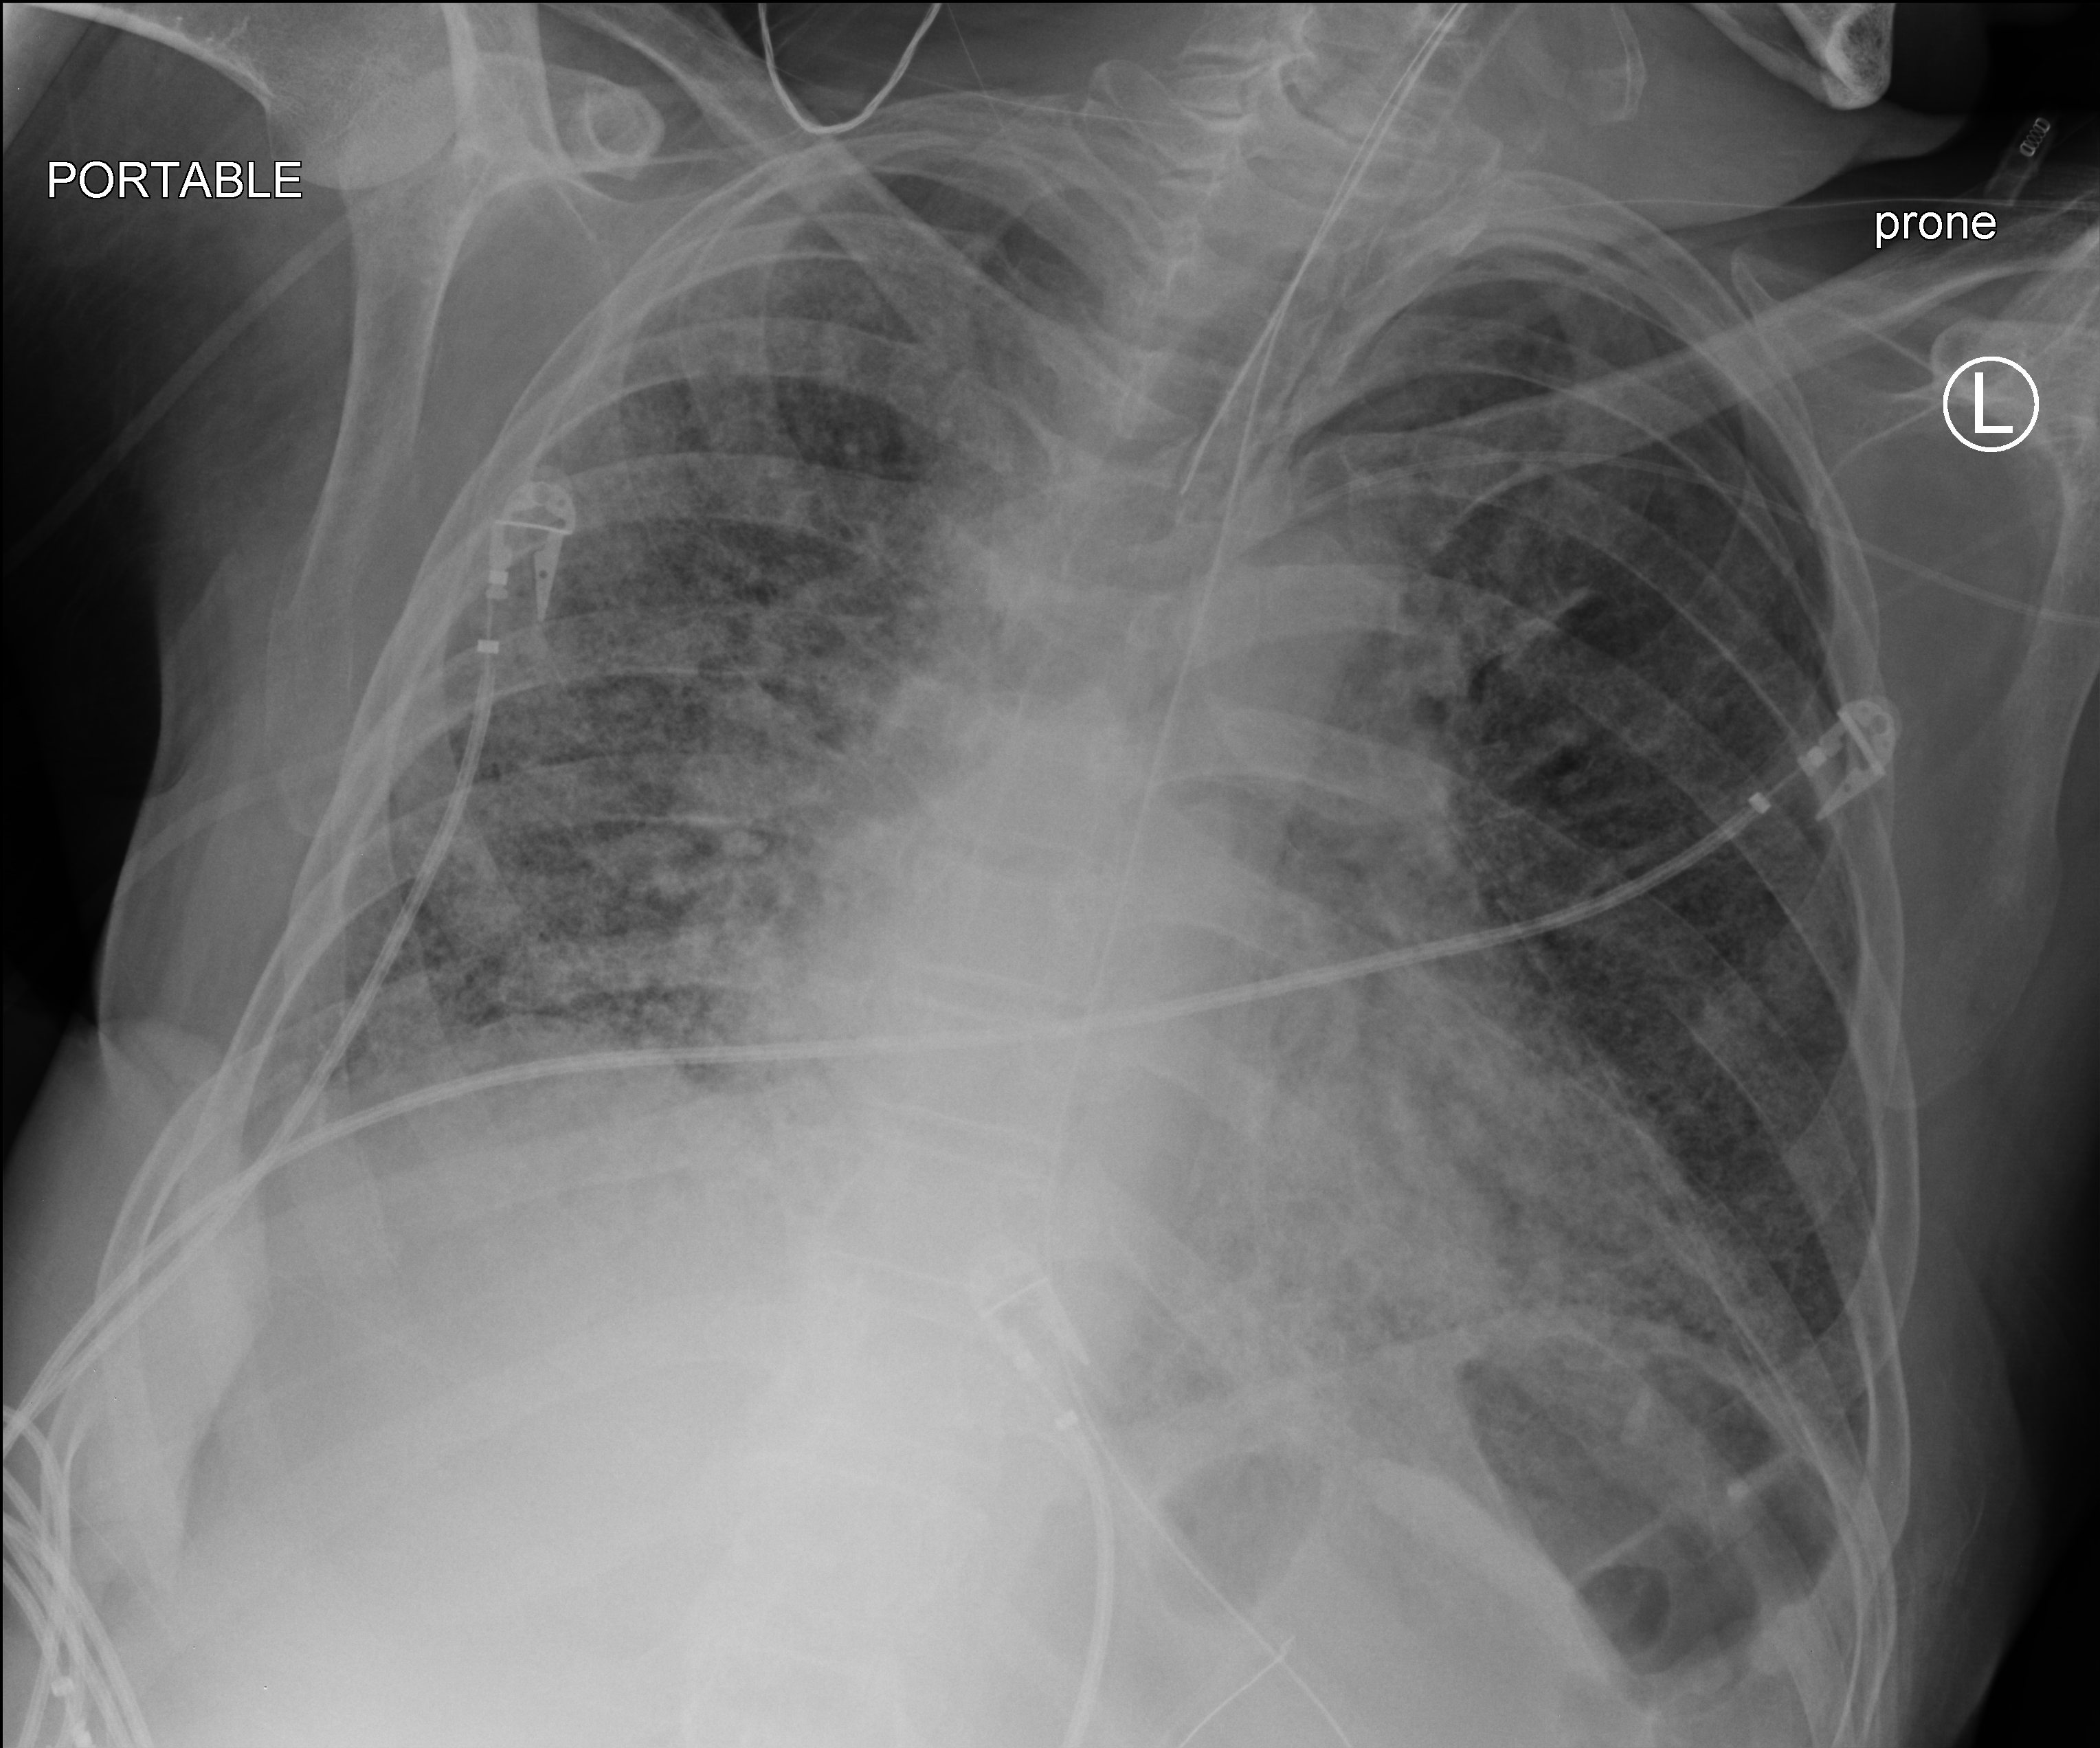
Portable chest radiograph; anteroposterior (AP) projection. Male patient hospitalised with COVID-19, age 60–74 years.
Admission-level facts for this patient (not findings on this image; timing relative to this image not recorded):
- admitted to intensive care during this hospital stay: yes
- mechanically ventilated during this hospital stay: yes